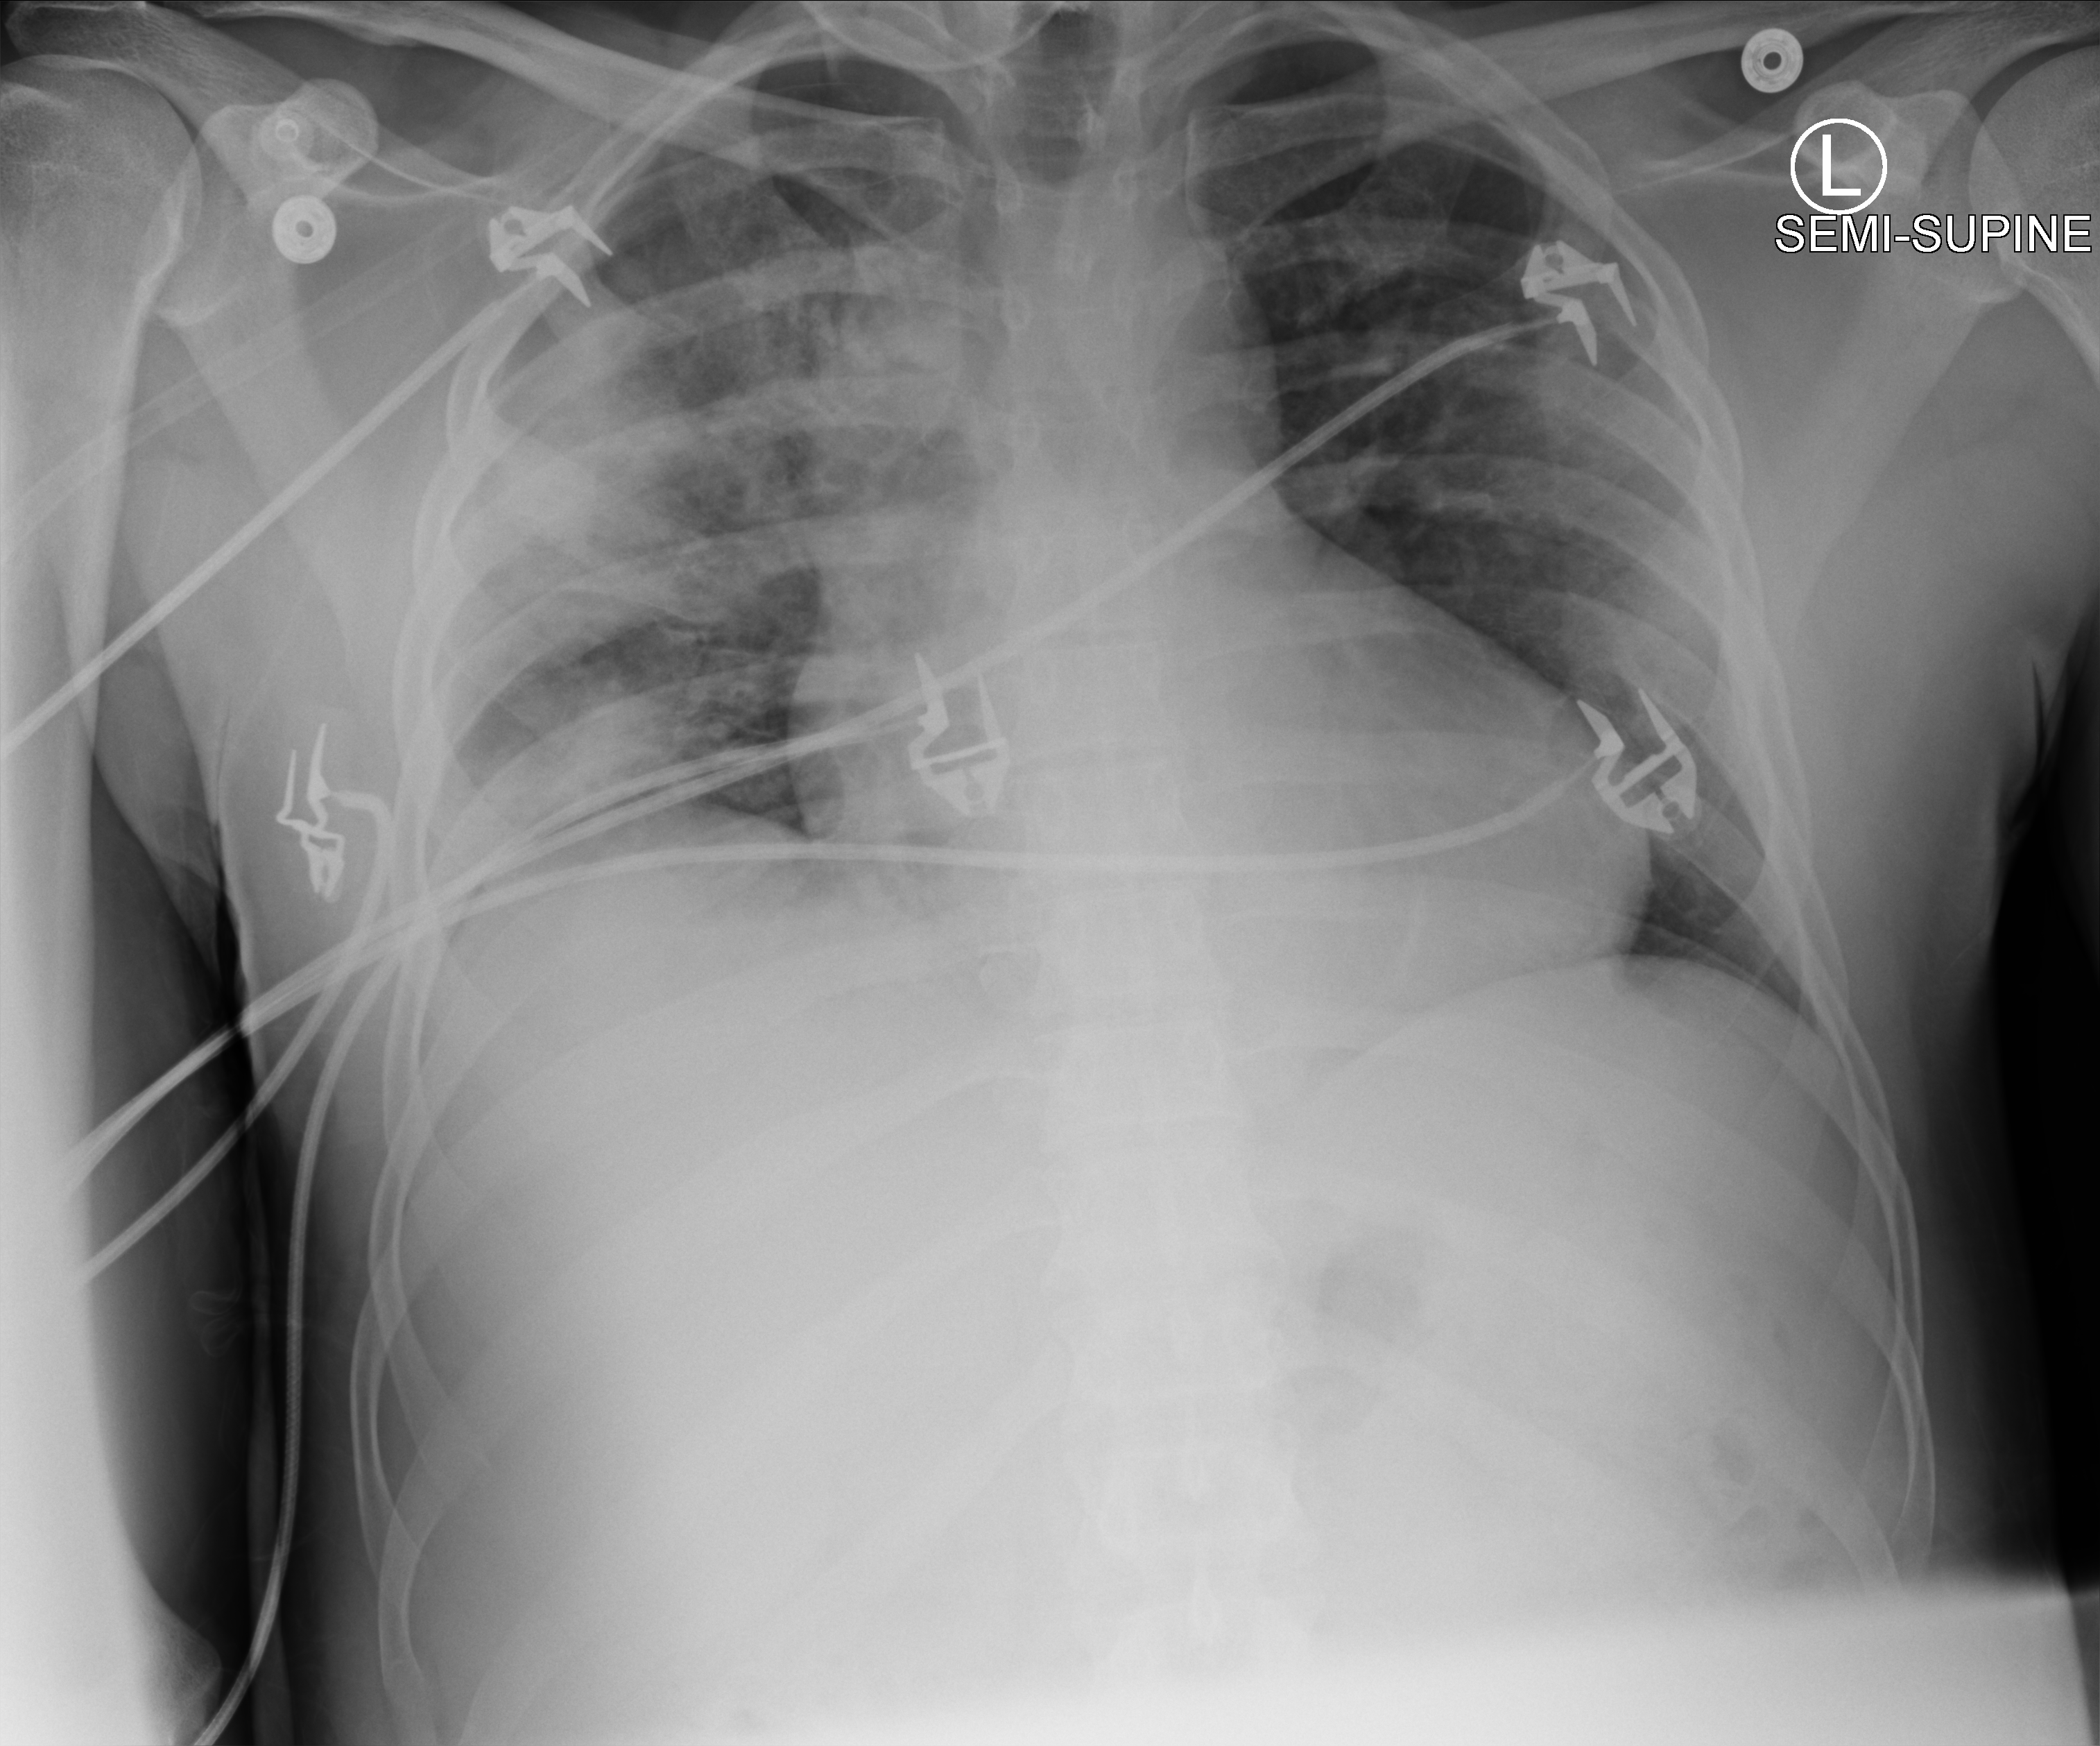
Chest X-ray (portable), anteroposterior (AP) projection. Male patient hospitalised with COVID-19, age 18–59 years.
Hospital-stay facts (about this admission, not read from this image; timing relative to this image not recorded): COPD (admission record): no; other chronic lung disease (admission record): no.